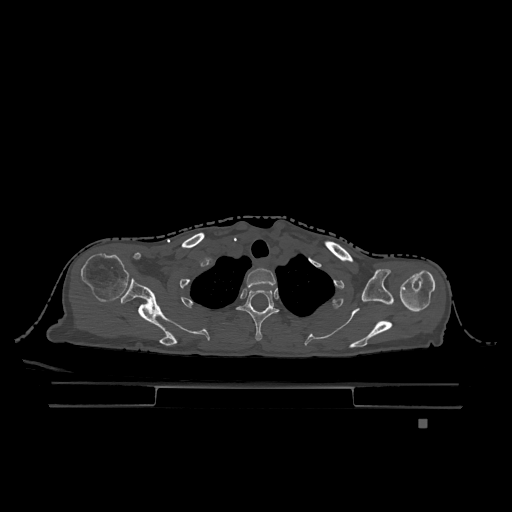
CT including the spine, one axial slice. Slice 966 of 1317 in the series (ordered by position). Bone window (W 1800 / L 400 HU). 512 × 512 image matrix, field of view 500 × 500 mm. Patient: female, 74 years. From the clinical record (not read from this slice): primary cancer: lung; vertebrae with lytic lesions (as recorded): T1, T4, T5, T6, L4, L5.
Annotated regions visible in this slice (semi-automatically segmented with operator editing):
- T1 vertebra: box from (x=246, y=268) to (x=276, y=289) px
- T2 vertebra: (x=237, y=289)–(x=278, y=341)